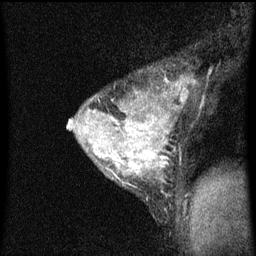
Breast MRI (dynamic contrast-enhanced), one sagittal slice. Position 47 of 60 along the scan axis. Dynamic contrast-enhanced series, image 2 of 3 at this slice position (ordered by acquisition). 1.5 T. TE 4.2 ms, TR 8 ms. 2 mm slice thickness. 256 × 256 image matrix, field of view 180 × 180 mm. Female patient, age 33 years.
Outlined on this slice (semi-automatic segmentation, software-assisted and operator-edited):
- analysis volume of interest (the breast-tissue region the enhancement analysis was run in; not a lesion): bounding box [x1, y1, x2, y2] px = [67, 72, 193, 215]
- tumour enhancement mask (voxels above the 70 % enhancement threshold inside the analysis volume of interest): [95, 104, 169, 177]